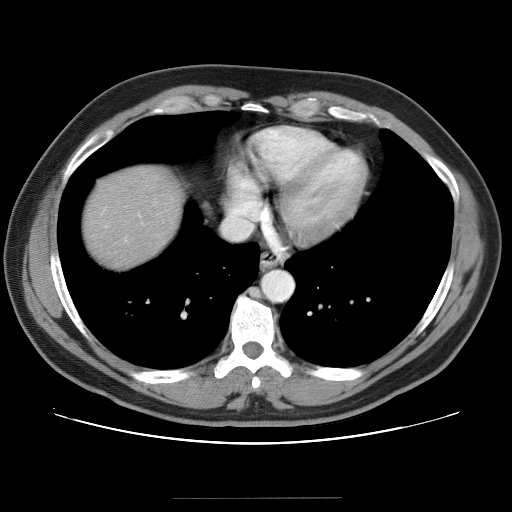
Contrast-enhanced abdominal CT (liver protocol), one axial slice. Position 36 of 40 along the scan axis. Reconstruction kernel STANDARD. 120 kVp. Soft-tissue window (W 400 / L 40 HU). 5 mm slice thickness. 512 × 512 image matrix, field of view 380 × 380 mm. Case-level facts recorded for this patient, not image findings: diagnosis: hepatocellular carcinoma (patient treated with transarterial chemoembolisation; whether this scan precedes or follows treatment is not stated here); TNM stage (as recorded): Stage-IVA; Child-Pugh class: B.
Annotated regions visible in this slice (semi-automatically segmented with operator editing):
- liver parenchyma outside the tumour (the mass and vessels are separate outlines, so this box may not span the whole liver): box from (x=84, y=166) to (x=182, y=266) px